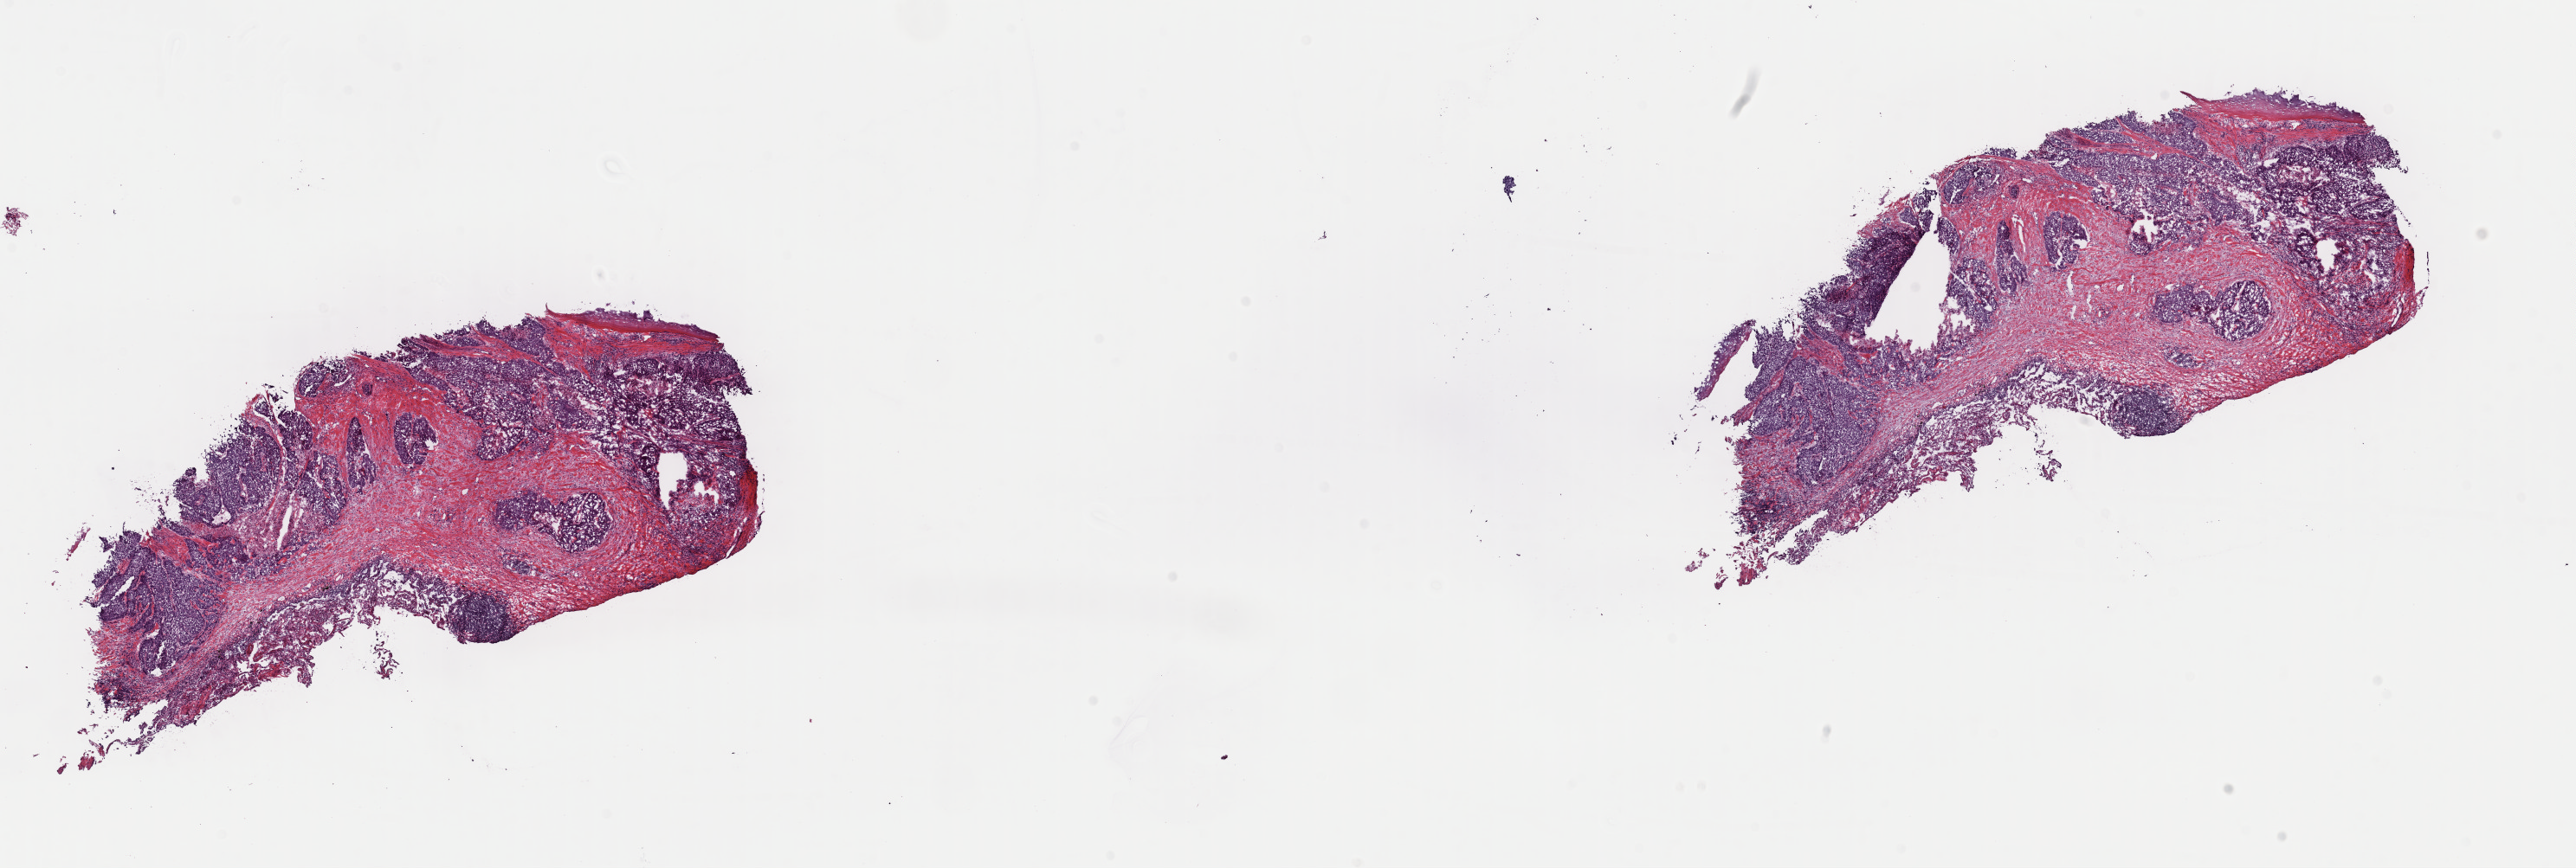
H&E-stained whole-slide image — low-resolution overview of the scanned area, about 23.5 x 7.9 mm. Frozen section from the top of the tissue portion. Sample: primary tumour, lung. Male, age 59 years at initial diagnosis. Composition of this section per pathologist review: tumour cells 35%, tumour nuclei 70%, normal cells 0%, stromal cells 60%, necrosis 5%. Infiltration values recorded for this section: lymphocyte infiltration 70%, monocyte infiltration 30%, neutrophil infiltration 0%.
Histologic diagnosis: Squamous cell carcinoma, NOS. Laterality: right. AJCC pathologic stage: IIIB.